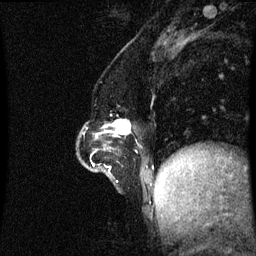
Breast MRI (dynamic contrast-enhanced), one sagittal slice; slice 21 of 60 in the series (ordered by position); dynamic contrast-enhanced series, image 2 of 3 at this slice position (ordered by acquisition); 1.5 T; TE 4.2 ms, TR 8.9 ms; 2.1 mm slice thickness; 256 × 256 image matrix, field of view 200 × 200 mm. Female patient, age 47 years. Case-level facts recorded for this patient, not image findings: setting: breast cancer imaged before/during neoadjuvant chemotherapy; receptor status: HR-positive, HER2-negative.
Annotated regions visible in this slice (semi-automatic segmentation, software-assisted and operator-edited):
- analysis volume of interest (the breast-tissue region the enhancement analysis was run in; not a lesion): box from (x=79, y=114) to (x=132, y=143) px
- tumour enhancement mask (voxels above the 70 % enhancement threshold inside the analysis volume of interest): (x=113, y=122)–(x=131, y=135)